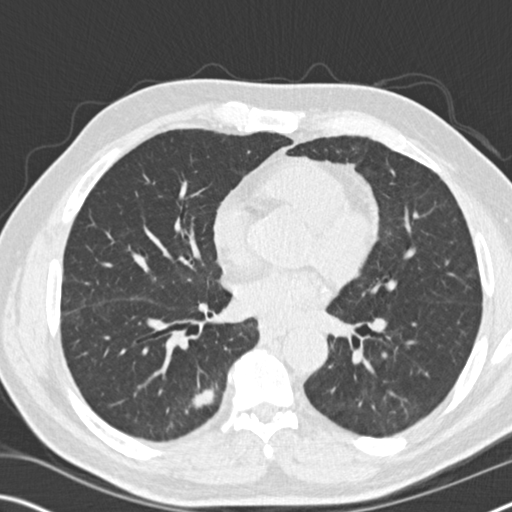
Low-dose screening chest CT, axial slice; baseline screening round; lung window (W 1500 / L -600 HU); 120 kVp; slice 90 of 169 in the series. Male participant, aged 71 years at enrolment. Current smoker at enrolment.
Lesion marked by an expert reader, bounding box [x1, y1, x2, y2] px = [159, 374, 229, 434]. The screening reader recorded 2 non-calcified nodules or masses ≥4 mm on this exam (right lower lobe, left lower lobe); which of them this box marks is not recorded. Official screen result: positive, change unspecified: nodule(s) >= 4 mm or enlarging nodule(s), mass(es), or other non-specific abnormalities suspicious for lung cancer. Later outcome: lung cancer diagnosed 215 days after this screen — squamous cell carcinoma, NOS, right lower lobe, moderately differentiated (G2), stage IB (AJCC 6th edition), 52 mm at pathology.